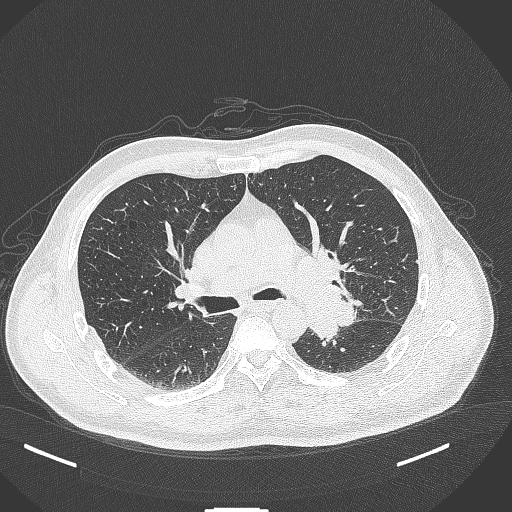
Chest CT, one axial slice; position 256 of 429 along the scan axis; reconstruction kernel B70f; 120 kVp; lung window (W 1500 / L -600 HU); 512 × 512 image matrix, field of view 400 × 400 mm. Male patient, age 55 years. From the clinical record (not read from this slice): clinical TNM (as recorded): T3 N0 M1c; histopathological grade: G3.
Structures marked on this image (rectangle marked by the reading radiologist):
- lung tumour (recorded histology: adenocarcinoma): bounding box (x1, y1, x2, y2) in pixels: (301, 286, 361, 346)